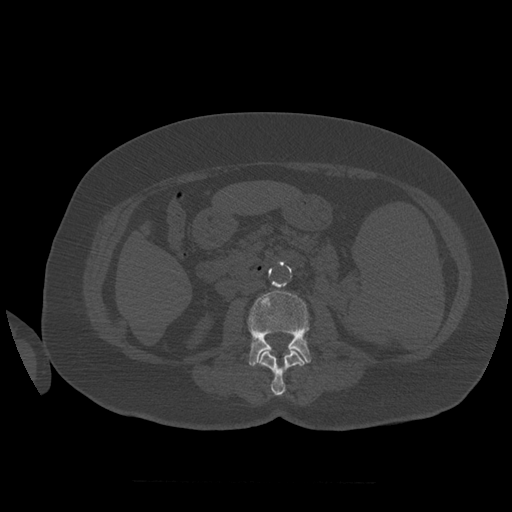
CT including the spine, one axial slice. Position 239 of 399 along the scan axis. Reconstruction kernel STANDARD. 120 kVp. Bone window (W 1800 / L 400 HU). 1.25 mm slice thickness. 512 × 512 image matrix, field of view 404 × 404 mm. Patient age 81 years. Case-level facts recorded for this patient, not image findings: primary cancer: renal; vertebrae with lytic lesions (as recorded): L1.
Outlined on this slice (semi-automatic segmentation, software-assisted and operator-edited):
- L2 vertebra: bounding box [x1, y1, x2, y2] px = [257, 346, 307, 396]
- L3 vertebra: [248, 289, 311, 366]